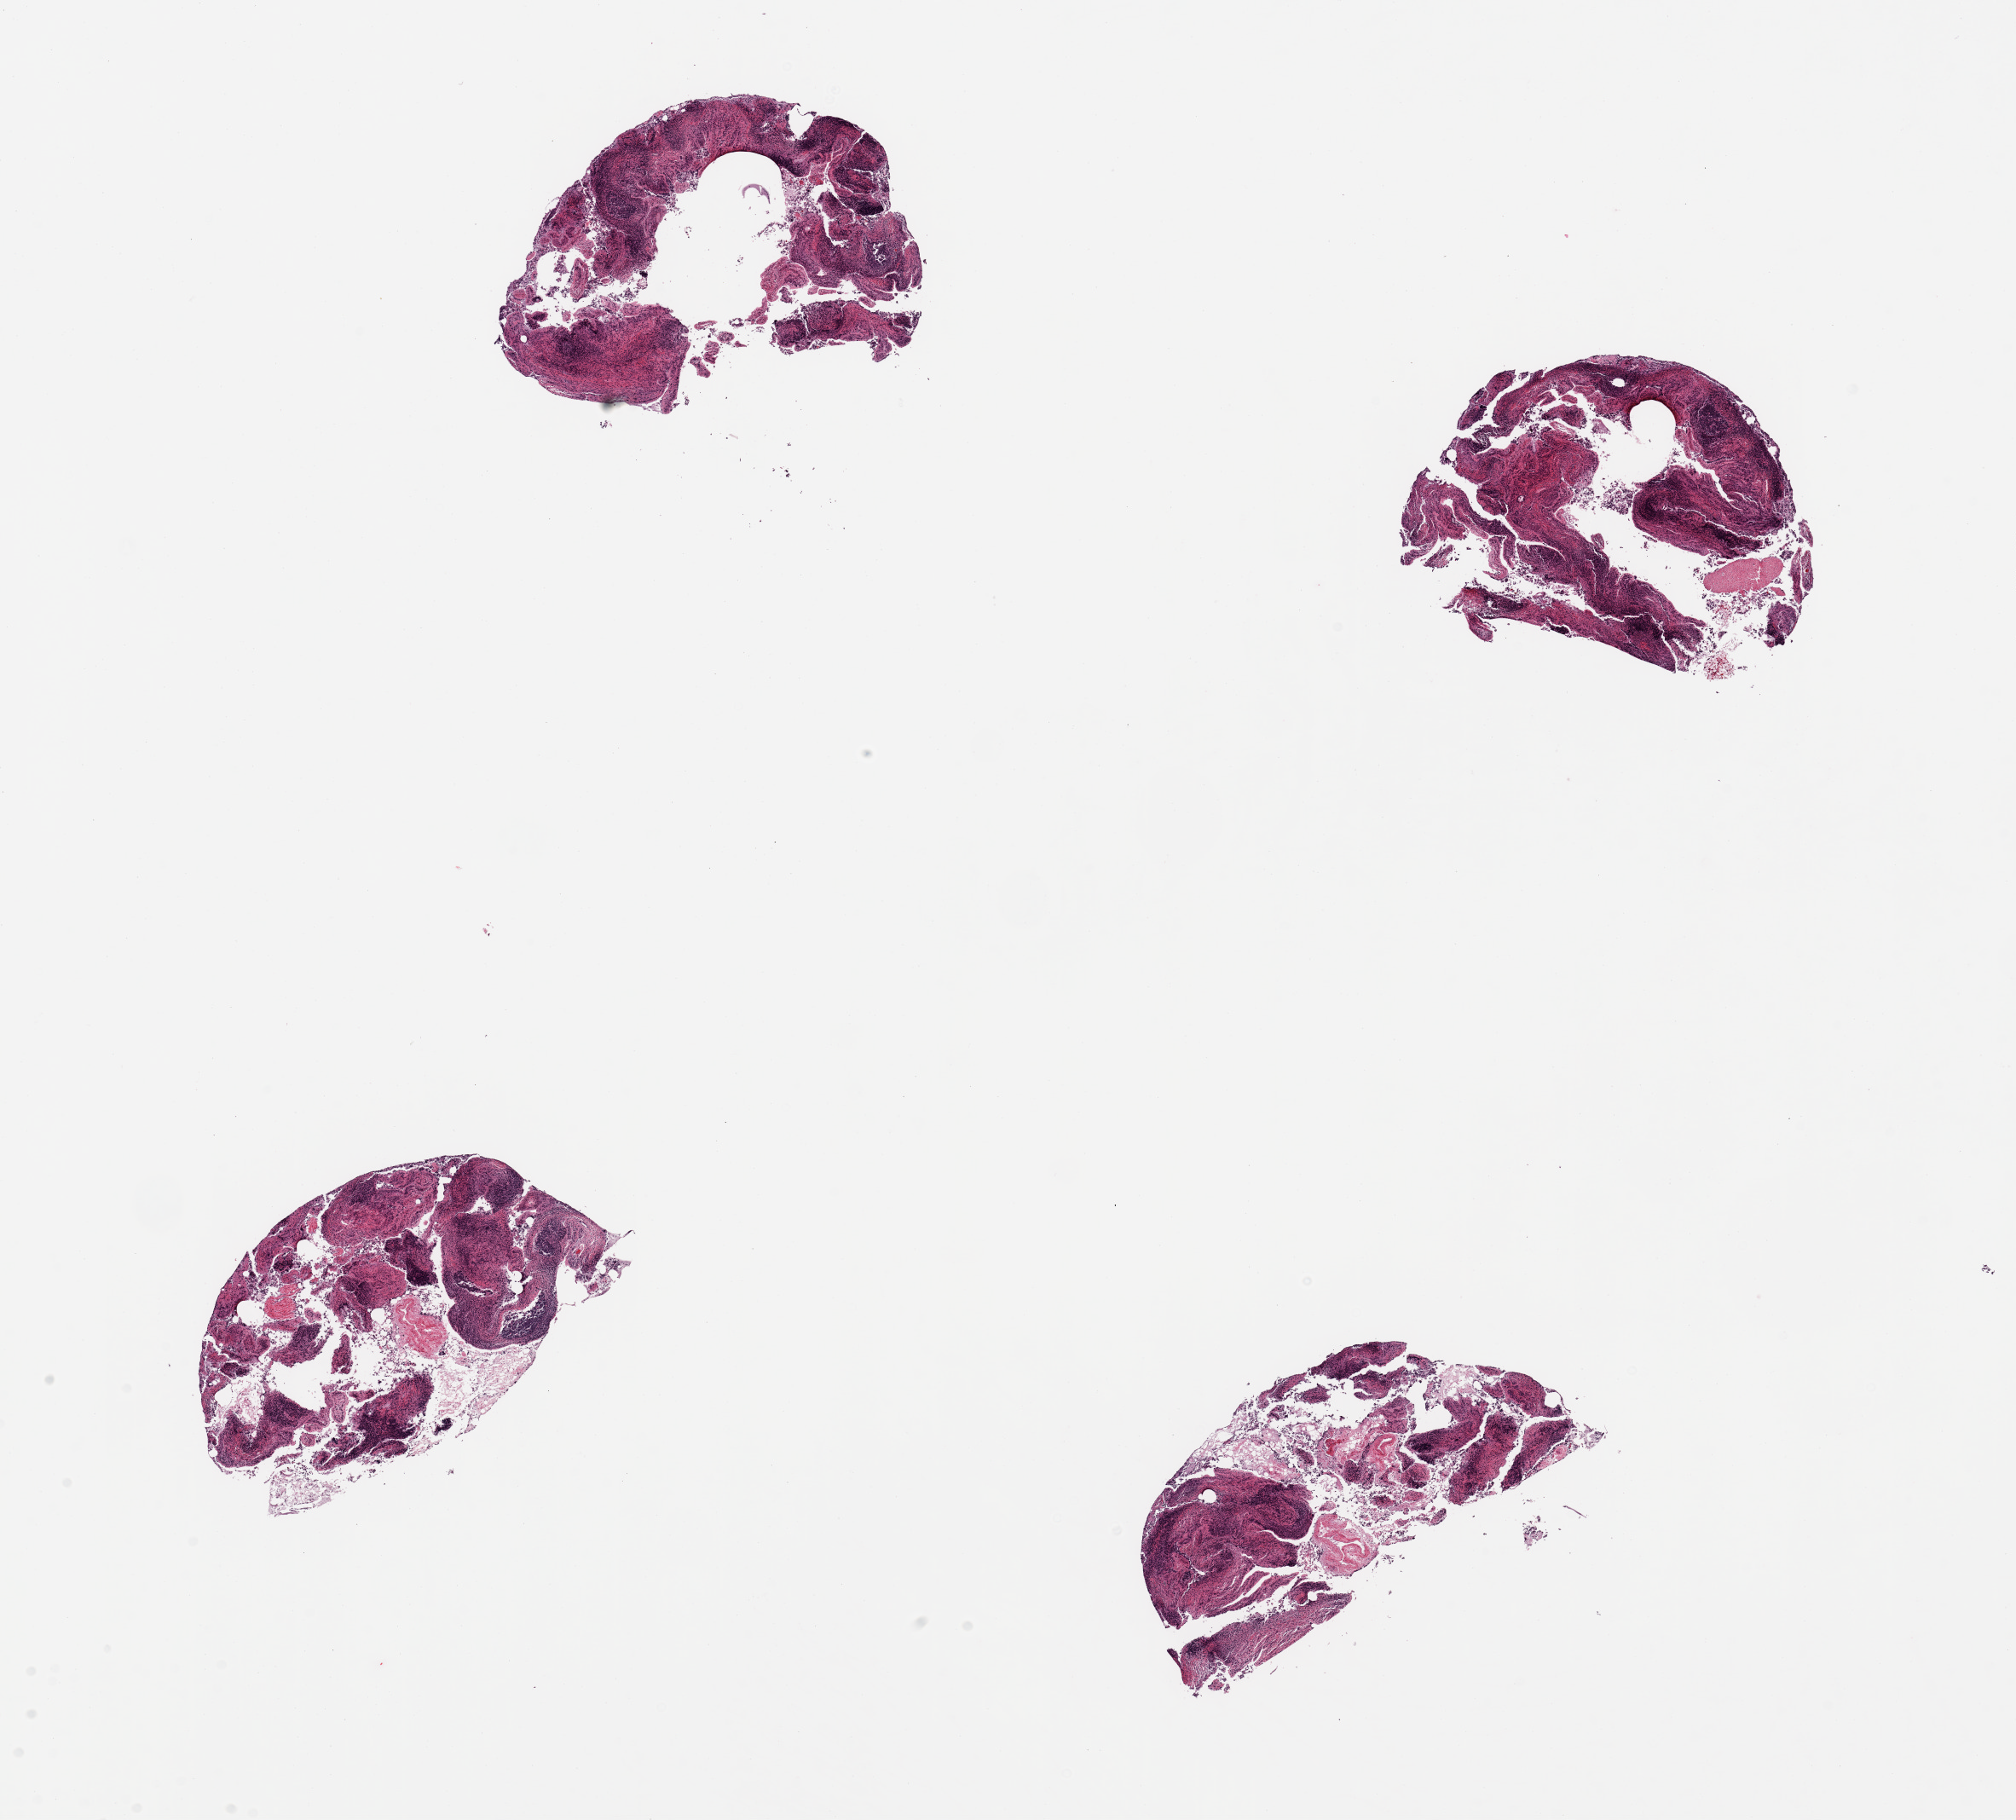
Digitized hematoxylin and eosin (H&E)-stained section, brightfield, a low-resolution overview of the entire scanned area, about 18.7 x 16.9 mm (from a 20x scan), PAXgene-fixed, paraffin-embedded tissue, target tissue: ileum, donor tissue sample.
Review note (as recorded): 4 pieces; lymphoid-rich fragmented mucosa.